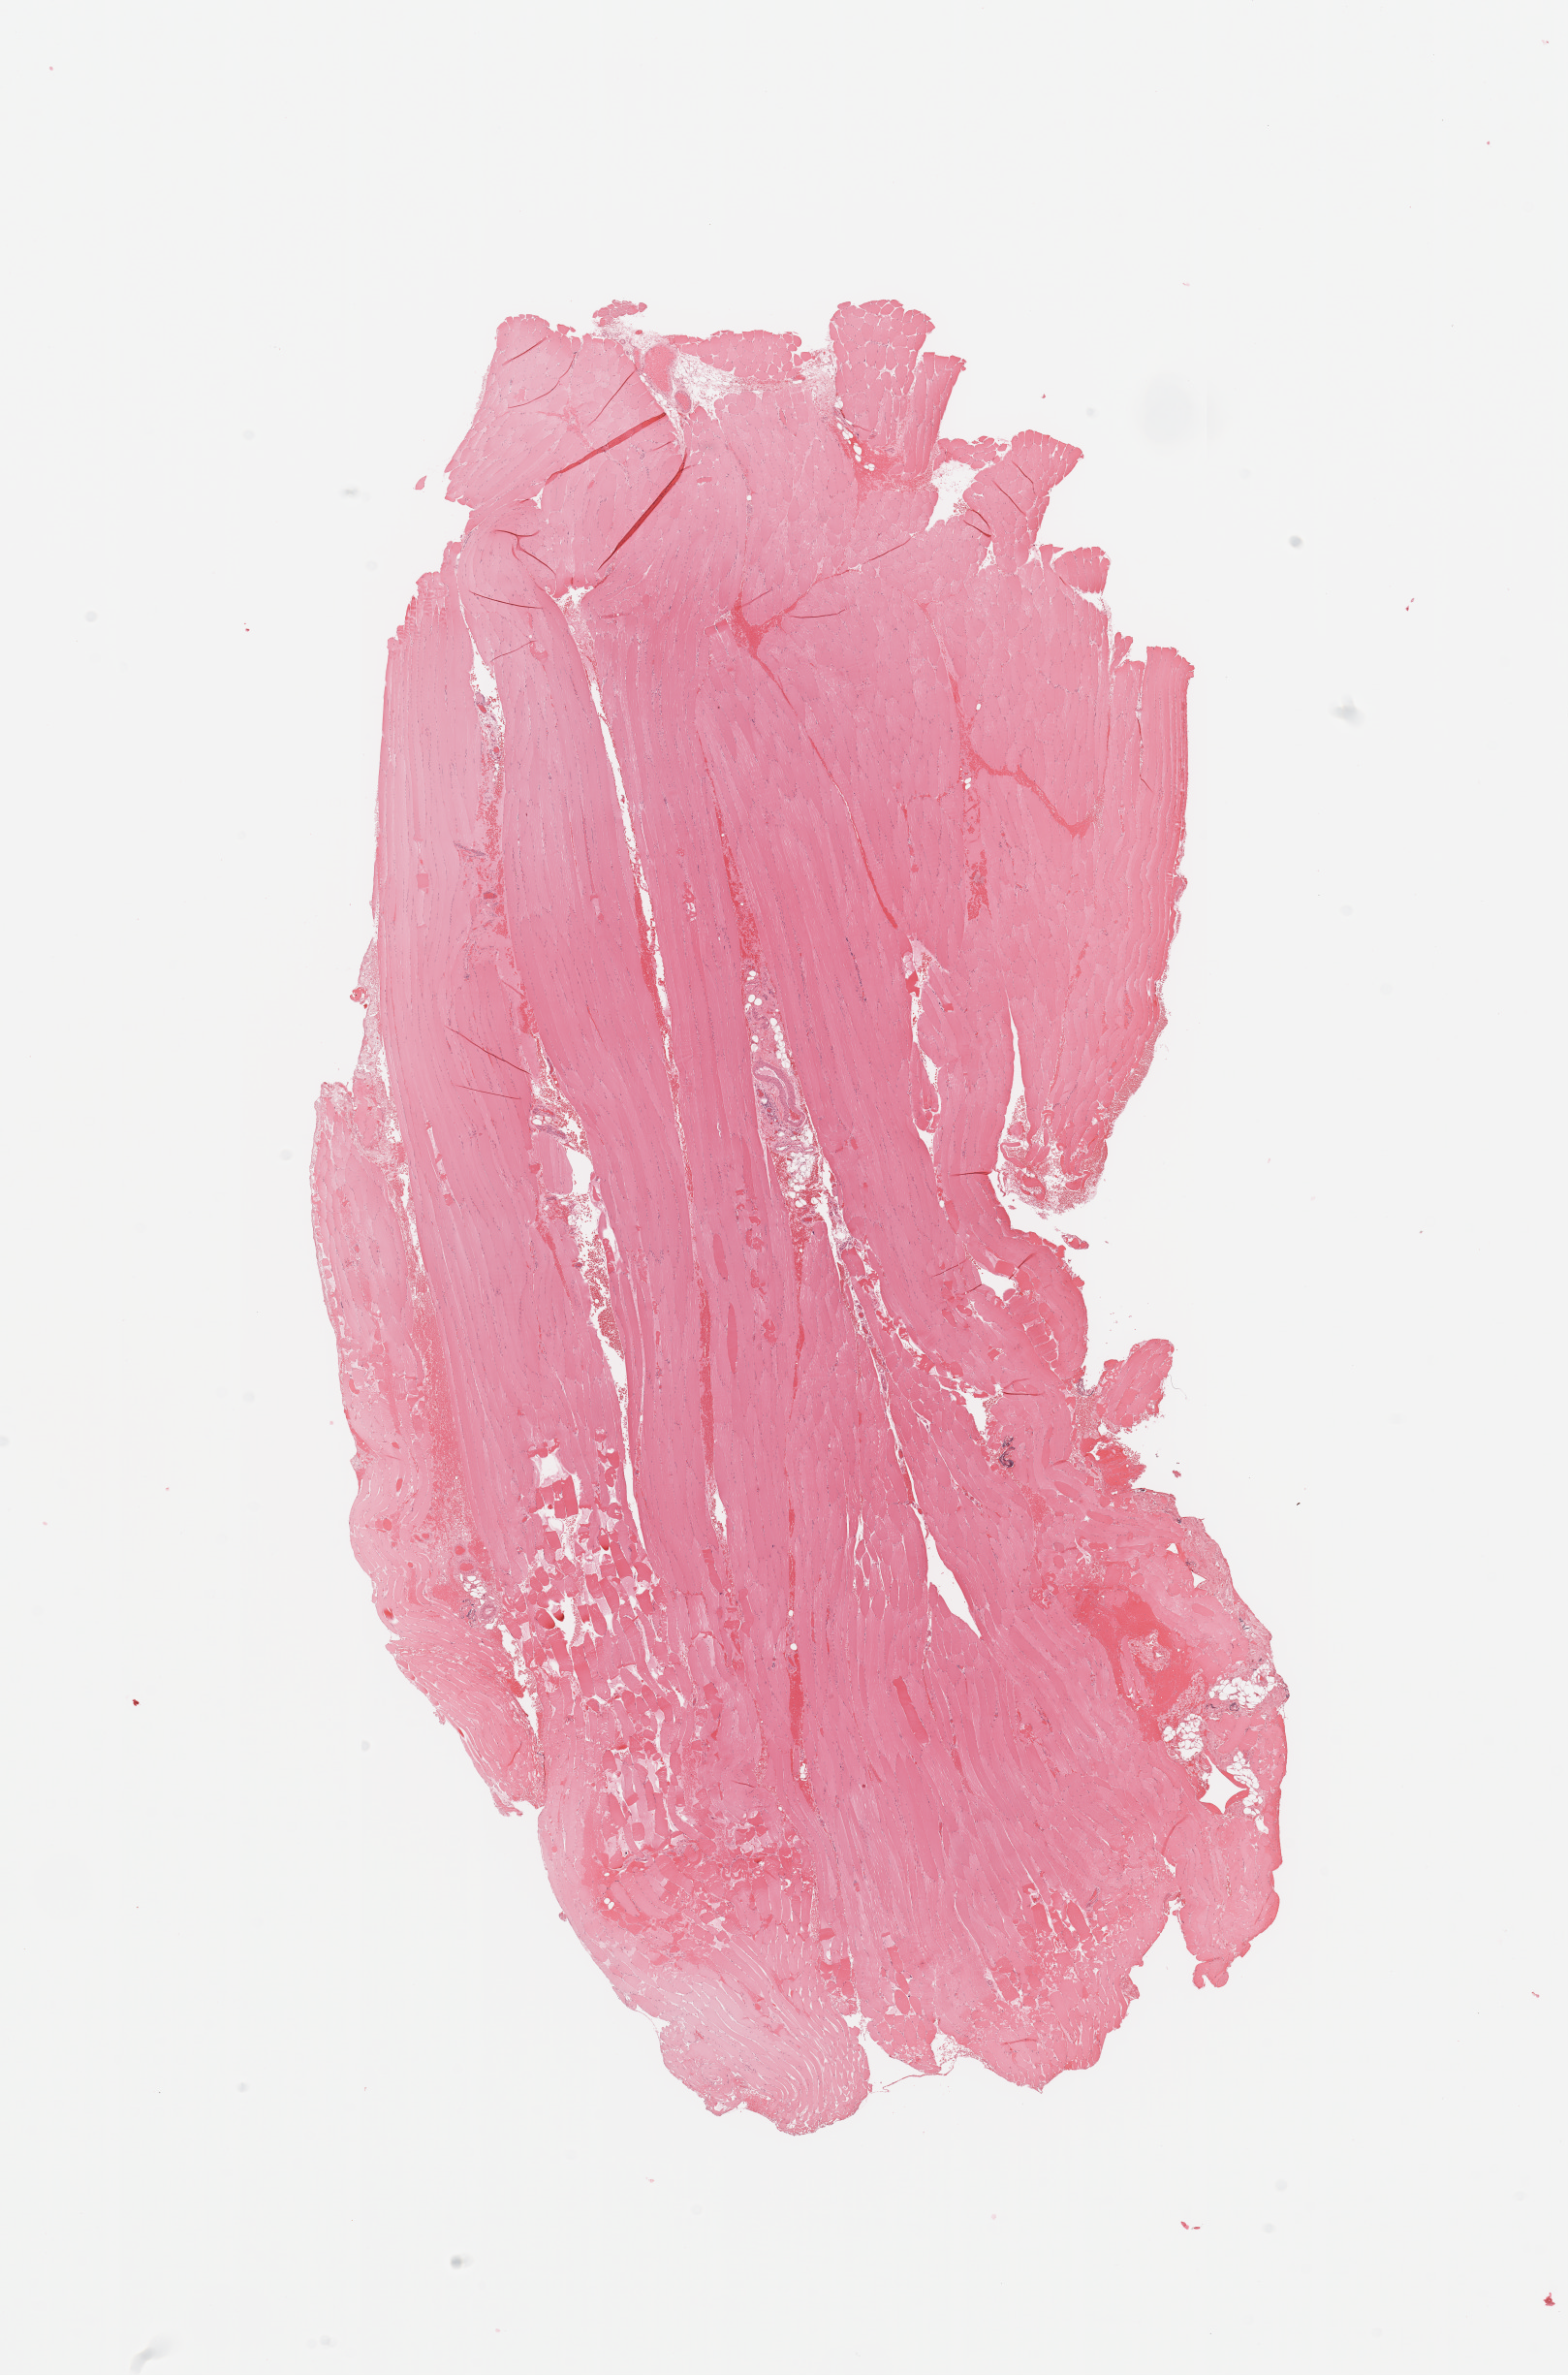
Hematoxylin and eosin (H&E) stained whole-slide image — shown as a low-resolution overview of the whole scanned area (about 12.8 x 19.4 mm); normal (non-tumour) tissue sample. Patient: male, age 78 years.
* this section: normal (non-tumour) tissue from the same patient
* patient diagnosis (cohort enrolment): sarcoma (site not recorded at cohort level)